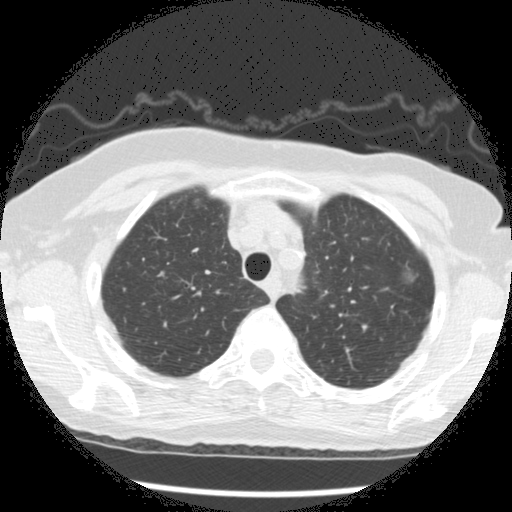
Chest CT (low-dose screening protocol), one axial image; second annual screen; lung window (W 1500 / L -600 HU); 2.5 mm slice thickness; slice 40 of 266 in the series. Female, age 73 years at enrolment. Former smoker at enrolment.
• Expert reader's lesion annotation, bounding box <392,245,433,287> (left, top, right, bottom; pixels).
• The screening reader recorded 3 non-calcified nodules or masses ≥4 mm on this exam (left upper lobe, left upper lobe, left upper lobe); which of them this box marks is not recorded.
• Official screen result: positive, change unspecified: nodule(s) >= 4 mm or enlarging nodule(s), mass(es), or other non-specific abnormalities suspicious for lung cancer.
• Participant outcome: lung cancer diagnosed 49 days after this screen — bronchiolo-alveolar adenocarcinoma, NOS, left upper lobe, well differentiated (G1), stage IA (AJCC 6th edition), 10 mm at pathology.